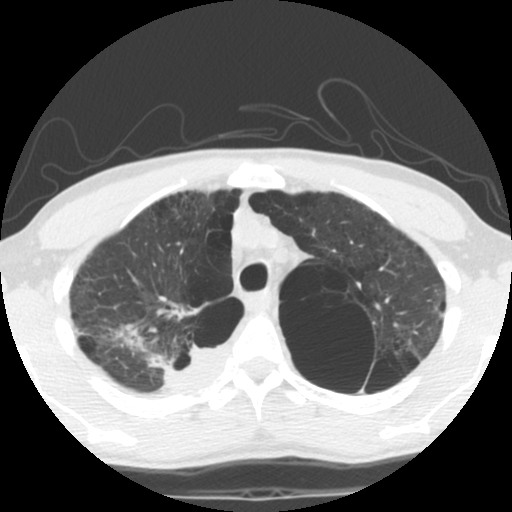
Low-dose screening chest CT, one axial slice; position 91 of 119 along the scan axis; reconstruction kernel STANDARD; 140 kVp; lung window (W 1500 / L -600 HU); 512 × 512 image matrix.
Outlined on this slice (outlined manually by an expert reader):
- lesion 1 (tumor, upper lobe of right lung): bounding box <115,322,228,390> (left, top, right, bottom; pixels)